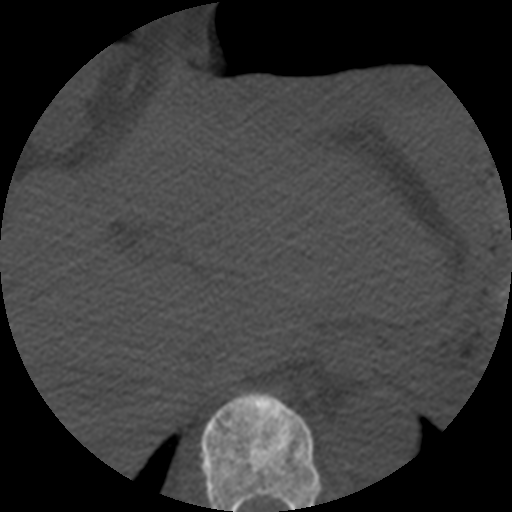
CT including the spine, one axial slice; position 267 of 508 along the scan axis; reconstruction kernel STANDARD; 120 kVp; bone window (W 1800 / L 400 HU); 1.25 mm slice thickness; 512 × 512 image matrix, field of view 160 × 160 mm. Patient age 57 years. Case-level facts recorded for this patient, not image findings: primary cancer: prostate.
Outlined on this slice (semi-automatic segmentation, software-assisted and operator-edited):
- T10 vertebra: bounding box <200,391,322,512> (left, top, right, bottom; pixels)